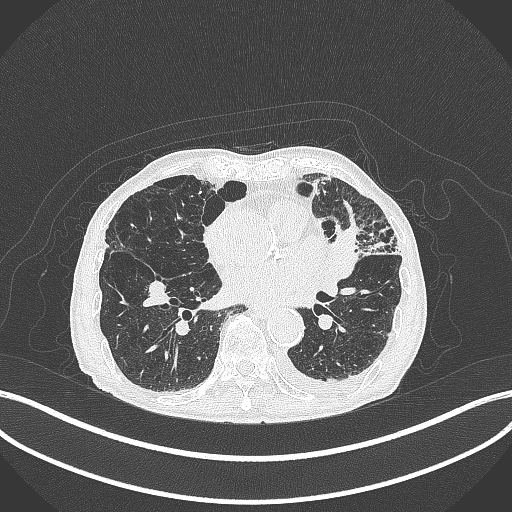
Chest CT, one axial slice. Position 162 of 385 along the scan axis. Reconstruction kernel B70f. 120 kVp. Lung window (W 1500 / L -600 HU). 1 mm slice thickness. 512 × 512 image matrix, field of view 400 × 400 mm. Male patient, age 90 years or older. Case-level facts recorded for this patient, not image findings: clinical TNM (as recorded): T2b N1 M0.
Outlined on this slice (bounding box drawn by a radiologist):
- lung tumour (recorded histology: squamous cell carcinoma): bounding box (x1, y1, x2, y2) in pixels: (323, 221, 365, 285)